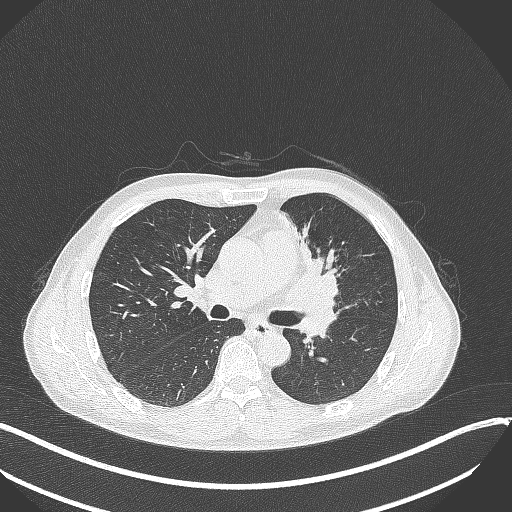
Chest CT, one axial slice; position 195 of 411 along the scan axis; reconstruction kernel B70f; 120 kVp; lung window (W 1500 / L -600 HU); 512 × 512 image matrix, field of view 400 × 400 mm. Male patient, age 56 years. From the clinical record (not read from this slice): clinical TNM (as recorded): T2a N0 M0.
Outlined on this slice (rectangle marked by the reading radiologist):
- lung tumour (recorded histology: squamous cell carcinoma): bounding box (x1, y1, x2, y2) in pixels: (279, 251, 351, 308)